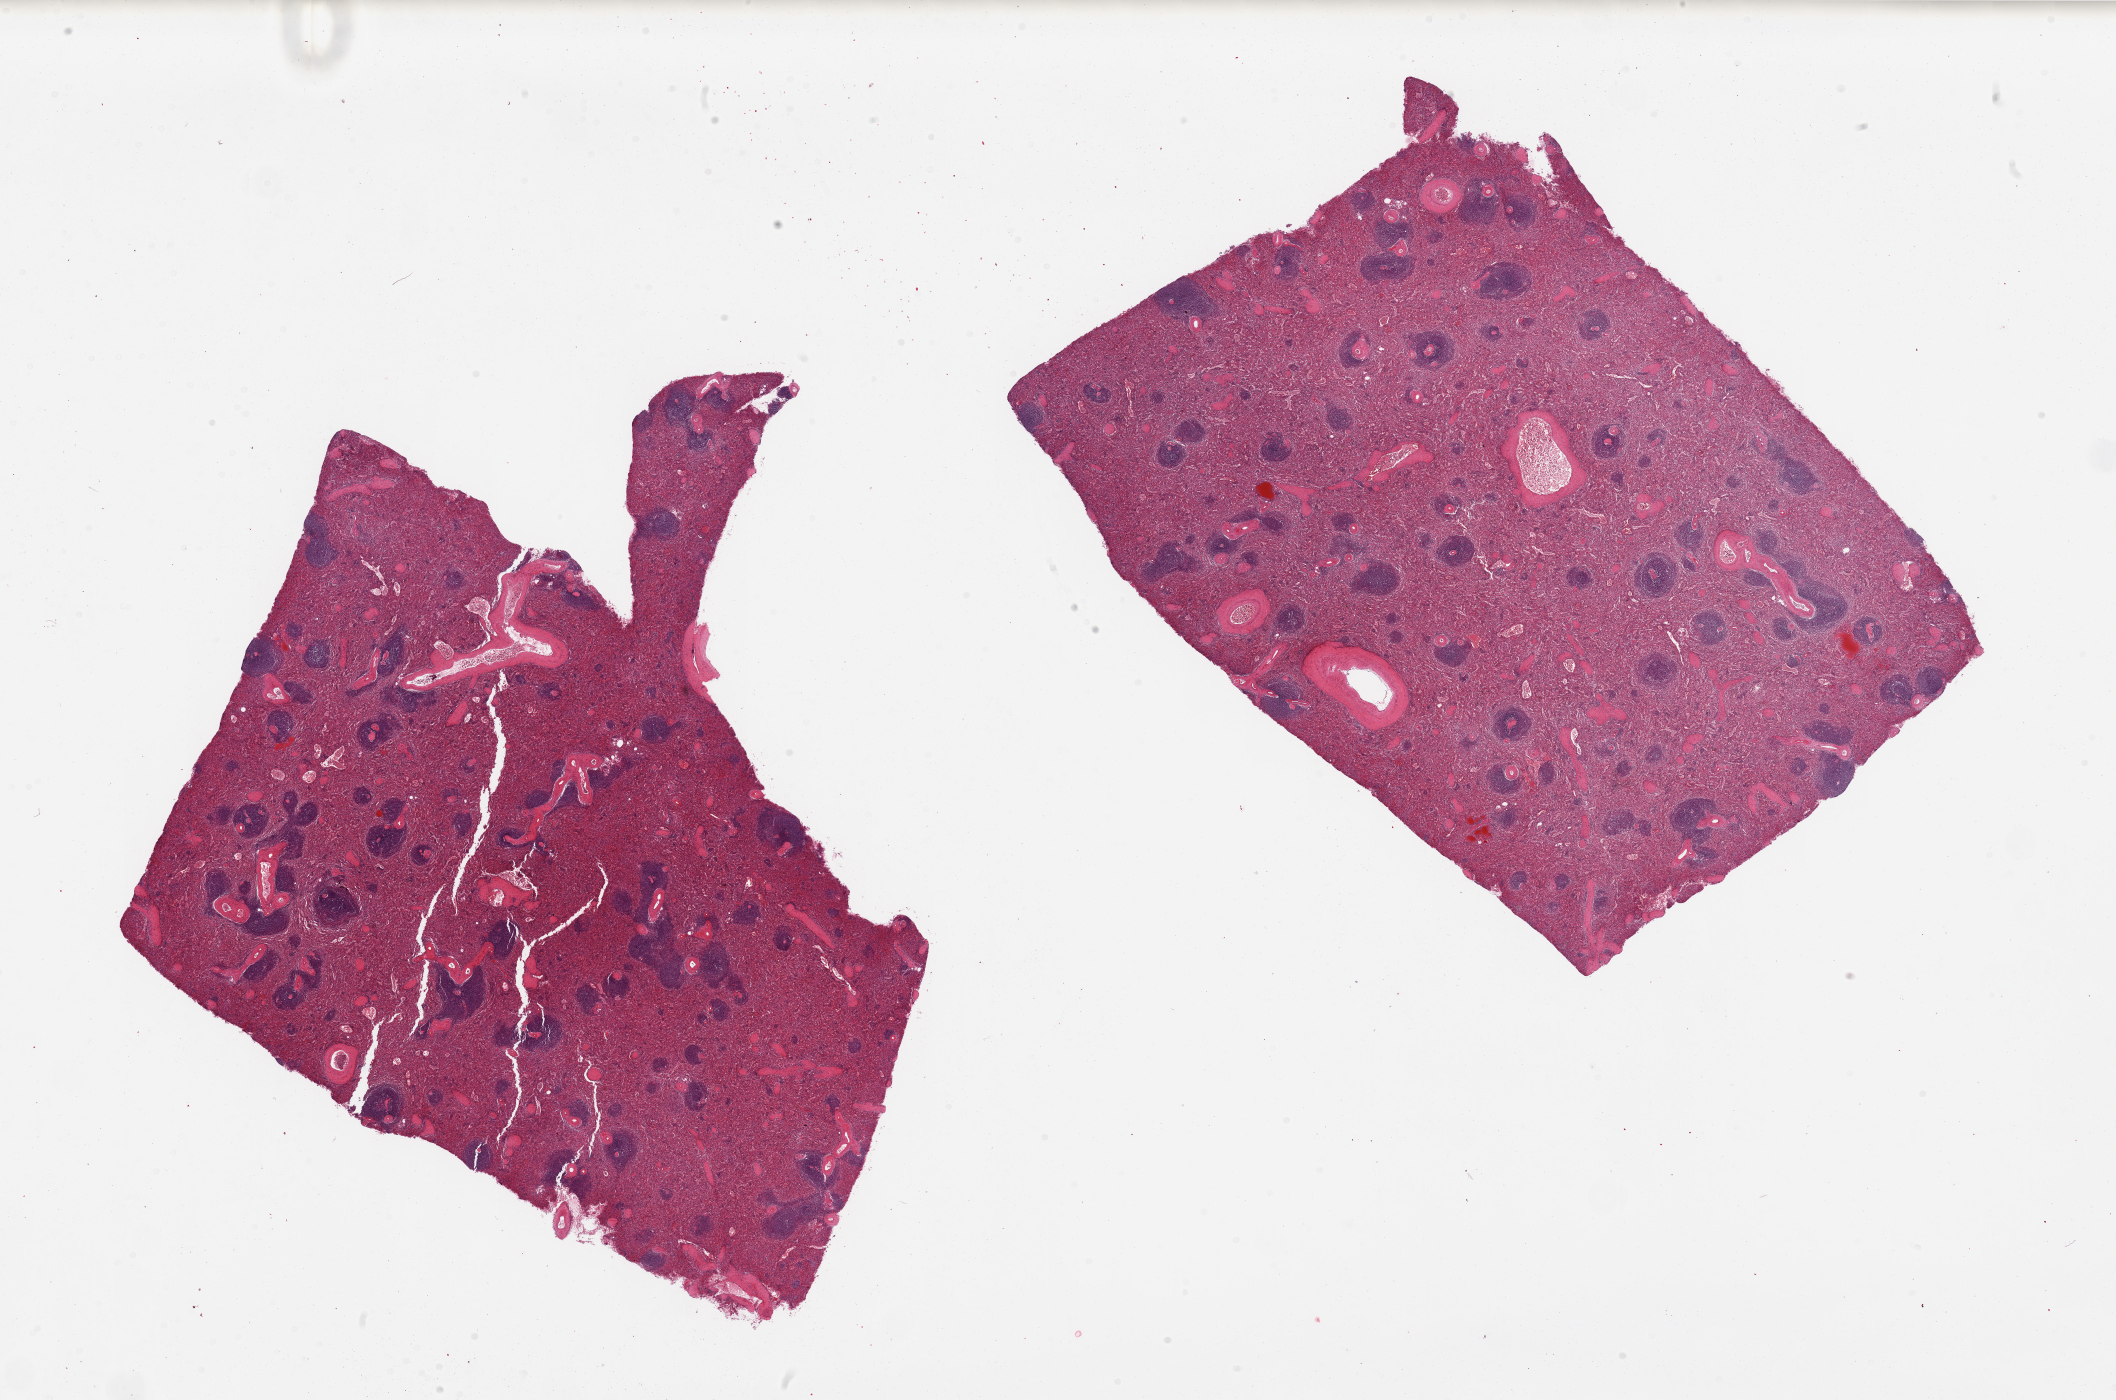
Whole-slide image, hematoxylin and eosin (H&E) stain — low-resolution overview of the scanned area, about 33.5 x 22.1 mm; PAXgene-fixed, paraffin-embedded tissue; sampled site (target tissue): spleen; donor tissue sample. Male donor.
Reviewer comment on this tissue sample: 2 pieces; not congested.